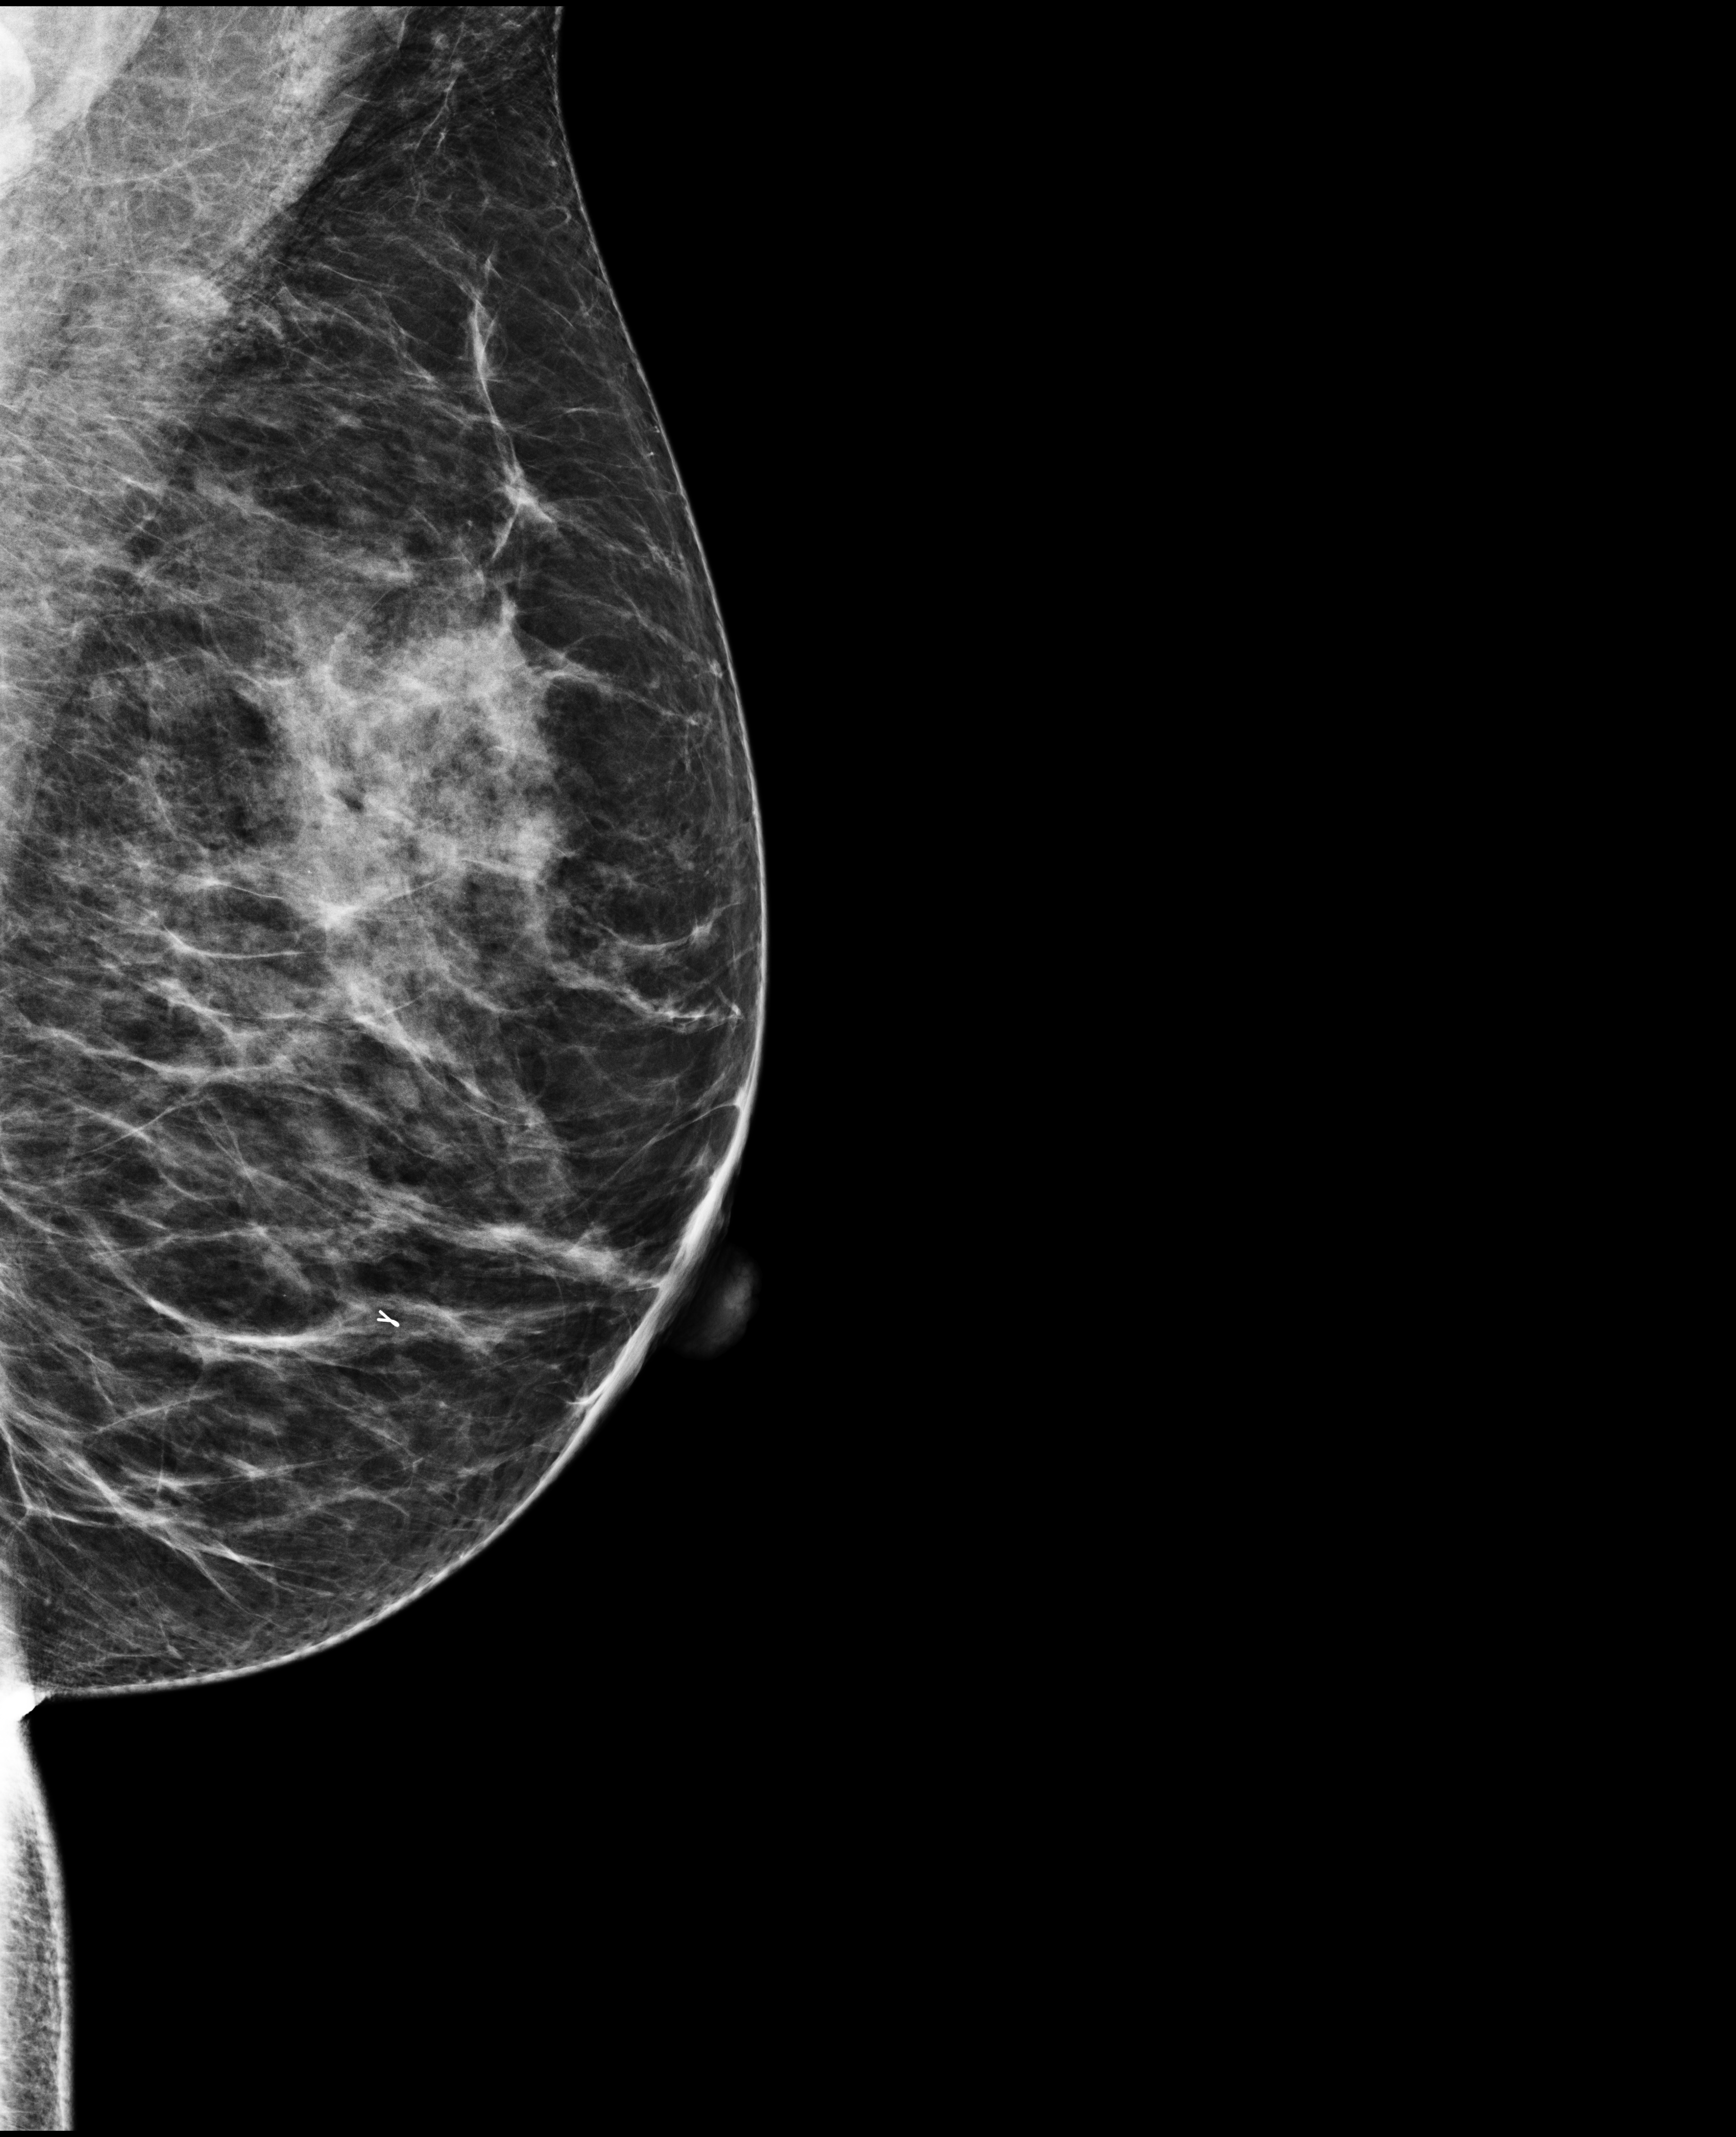
Screening examination, compressed breast thickness 61 mm, system: Selenia Dimensions.
Image type: full-field digital mammogram. Breast: left. Projection: mediolateral oblique (MLO) view.